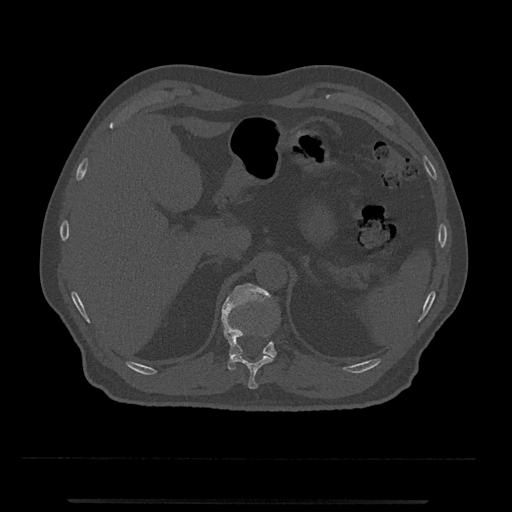
CT including the spine, one axial slice. Slice 433 of 797 in the series (ordered by position). Reconstruction kernel Br40s/3. Bone window (W 1800 / L 400 HU). 0.5 mm slice thickness. 512 × 512 image matrix. Patient: male, 63 years. From the clinical record (not read from this slice): primary cancer: prostate.
Outlined on this slice (semi-automatic segmentation, software-assisted and operator-edited):
- T11 vertebra: bounding box (x1, y1, x2, y2) in pixels: (233, 354, 274, 389)
- T12 vertebra: (221, 283, 277, 371)